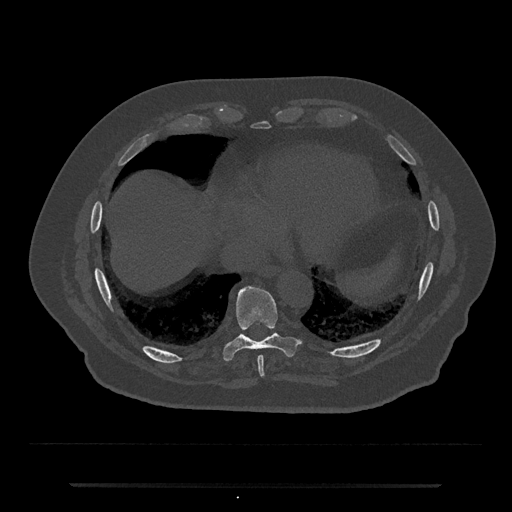
CT including the spine, one axial slice; slice 761 of 797 in the series (ordered by position); 120 kVp; bone window (W 1800 / L 400 HU); 0.5 mm slice thickness; 512 × 512 image matrix. Patient: male, 80 years. From the clinical record (not read from this slice): primary cancer: prostate.
Annotated regions visible in this slice (semi-automatically segmented with operator editing):
- T8 vertebra: bounding box (x1, y1, x2, y2) in pixels: (257, 356, 265, 378)
- T9 vertebra: (223, 284, 299, 361)